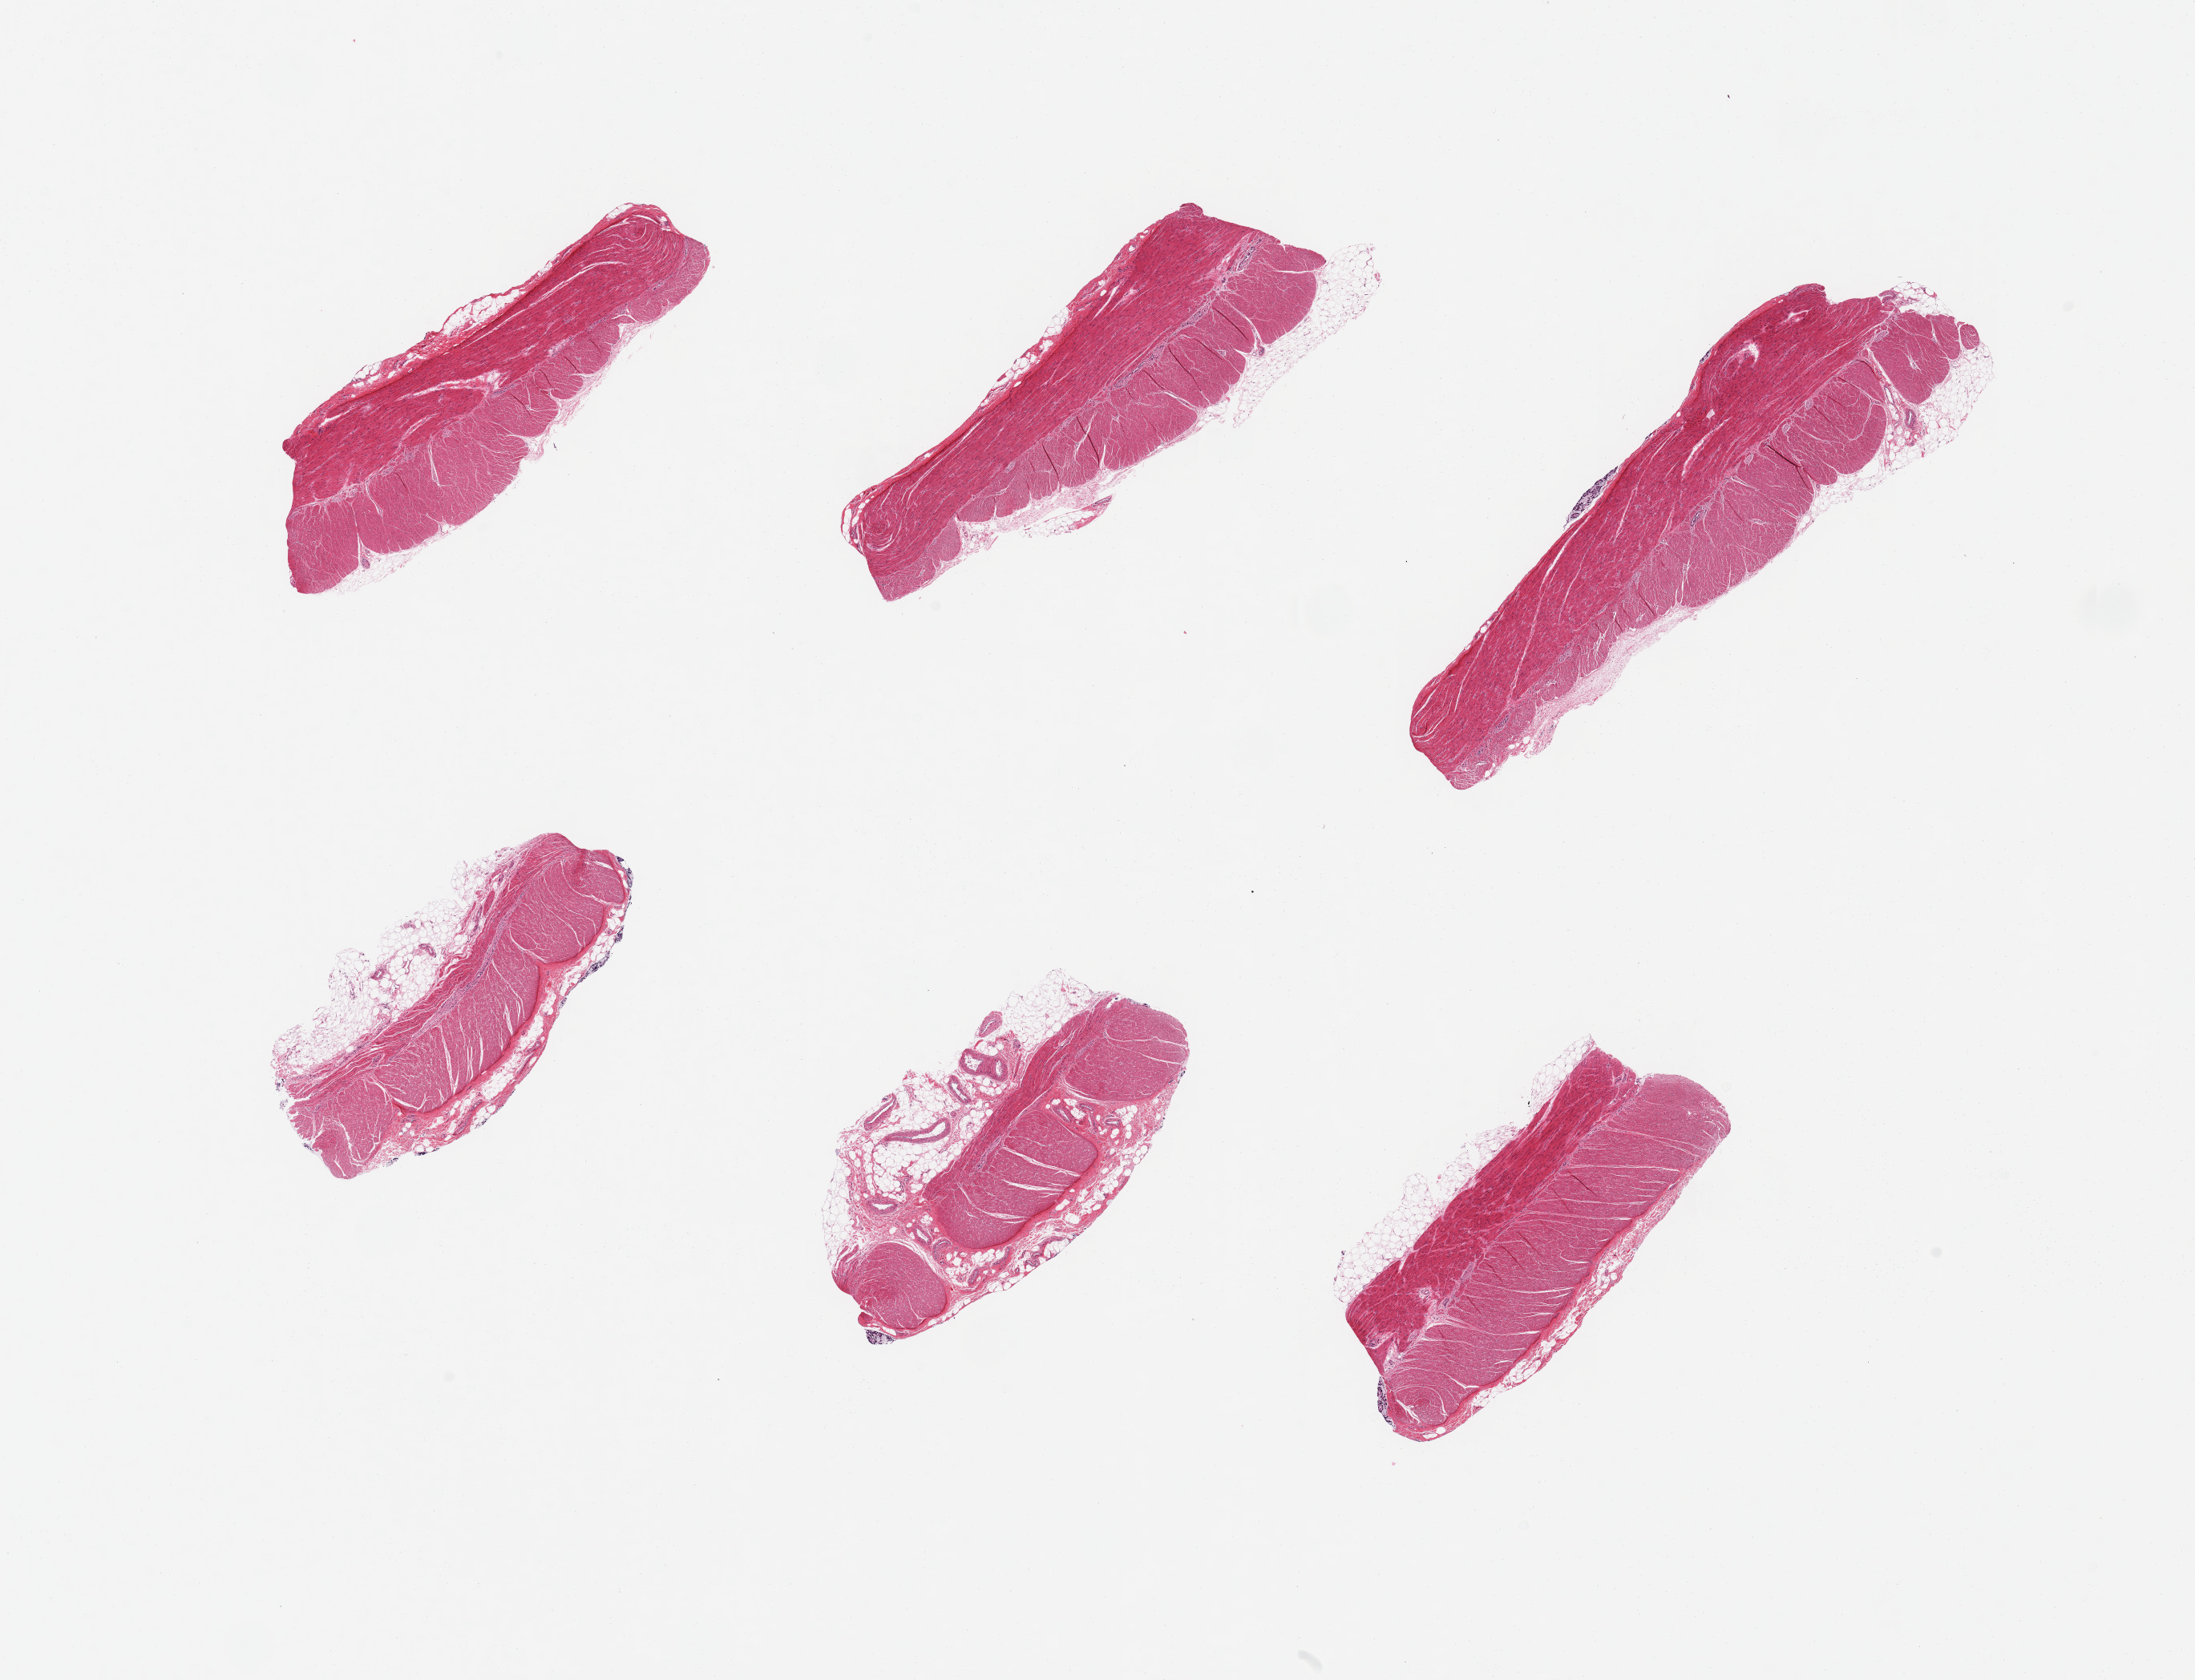
Whole-slide image, H&E stain — low-resolution overview of the scanned area, about 21.7 x 16.6 mm. PAXgene-fixed, paraffin-embedded tissue. Sampled site (target tissue): sigmoid colon. Donor tissue sample. Donor: male.
Pathologist's review note for this sample: 6 pieces; muscularis; abundant adjacent fat on 2.